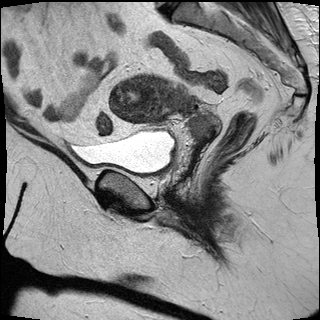
Pelvic MRI for cervical cancer, one sagittal slice. Position 17 of 30 along the scan axis. T2-weighted. 1.5 T. TE 89 ms, TR 2930 ms. 4 mm slice thickness. 320 × 320 image matrix, field of view 260 × 260 mm. Patient: female, 53 years.
Structures marked on this image (expert manual segmentation):
- uterus and cervix: bounding box <109,75,214,138> (left, top, right, bottom; pixels)